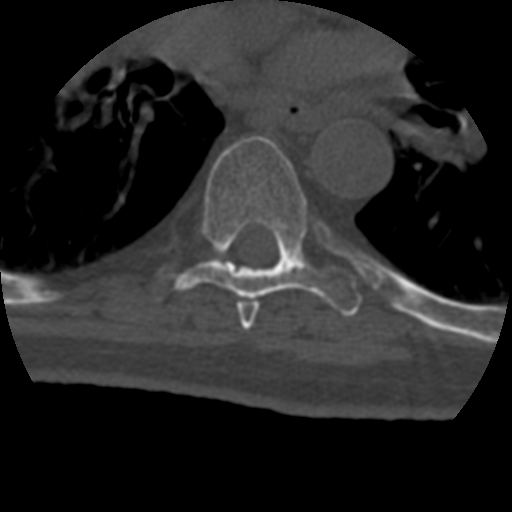
CT including the spine, one axial slice; position 283 of 399 along the scan axis; bone window (W 1800 / L 400 HU); 512 × 512 image matrix, field of view 160 × 160 mm. Patient age 69 years. From the clinical record (not read from this slice): primary cancer: prostate.
Annotated regions visible in this slice (semi-automatically segmented with operator editing):
- T6 vertebra: bounding box [x1, y1, x2, y2] px = [237, 301, 258, 331]
- T7 vertebra: [151, 136, 362, 316]